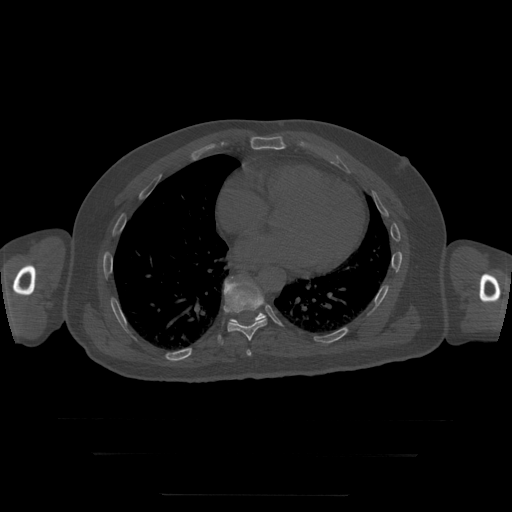
CT including the spine, one axial slice; slice 140 of 397 in the series (ordered by position); reconstruction kernel STANDARD; 120 kVp; bone window (W 1800 / L 400 HU); 1.25 mm slice thickness; 512 × 512 image matrix, field of view 510 × 510 mm. Patient age 73 years. From the clinical record (not read from this slice): primary cancer: prostate.
Structures marked on this image (semi-automatic segmentation, software-assisted and operator-edited):
- T10 vertebra: box from (x=225, y=283) to (x=266, y=324) px
- T8 vertebra: (x=247, y=350)–(x=252, y=356)
- T9 vertebra: (x=218, y=282)–(x=267, y=344)